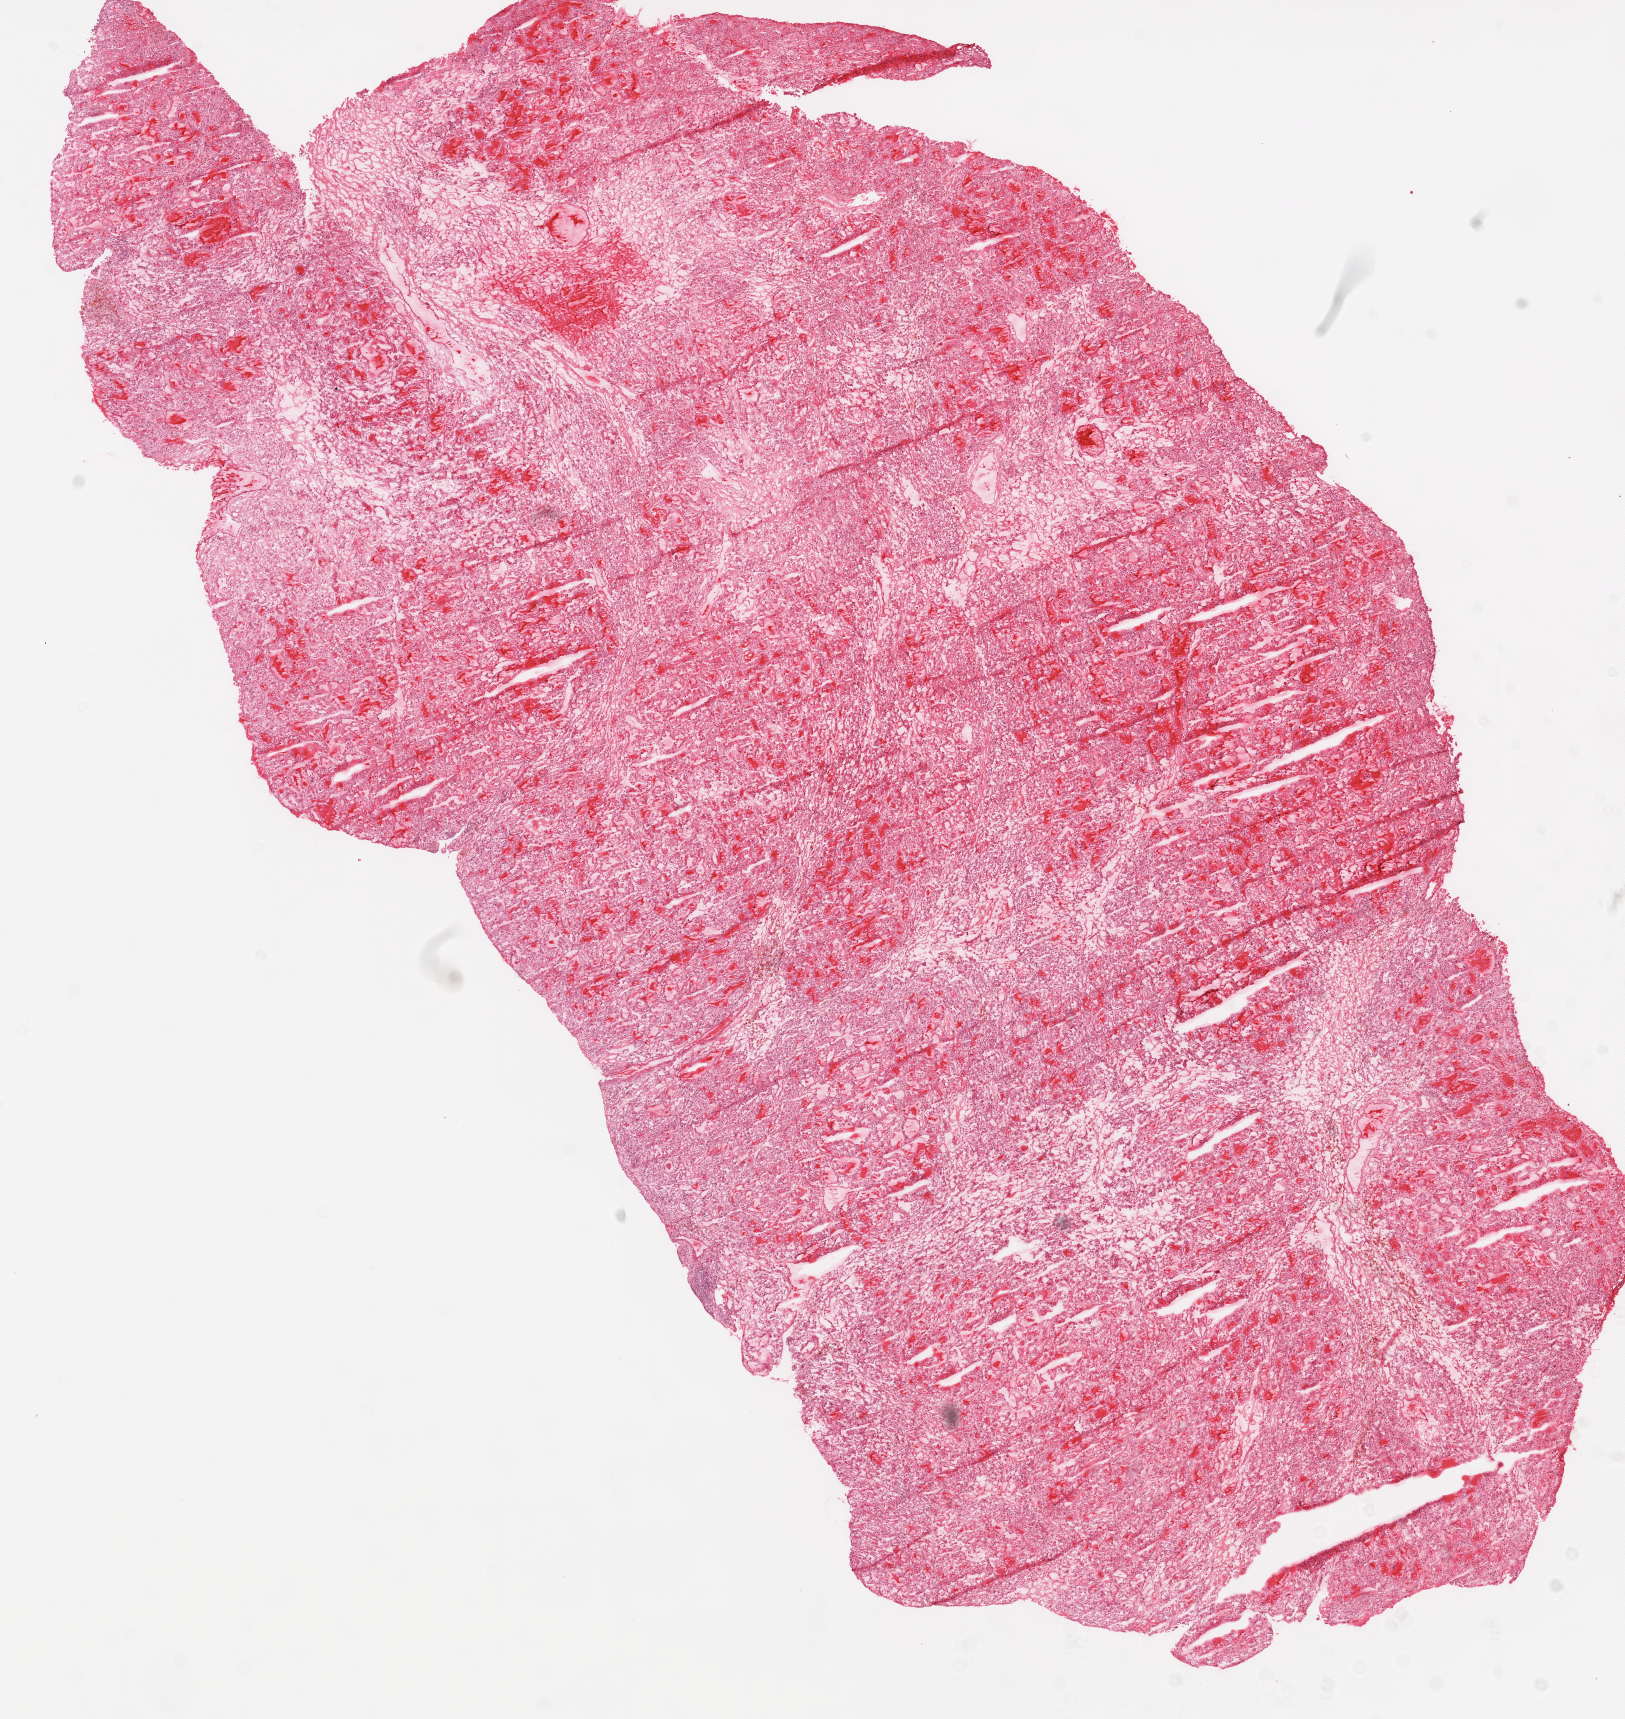
Whole-slide histology image, H&E-stained — a low-resolution overview of the entire scanned area, about 13.0 x 13.8 mm (slide scanned at 20x), frozen section from the top of the tissue portion, primary tumour sample from the kidney. Patient: male, age at initial diagnosis 62 years. Histologic grade: G4 (undifferentiated). Composition of this section per pathologist review: tumour cells 90%, tumour nuclei 90%, normal cells 0%, stromal cells 10%, necrosis 0%.
Laterality: right. AJCC pathologic stage: III (6th edition). Histologic diagnosis: Clear cell adenocarcinoma, NOS.